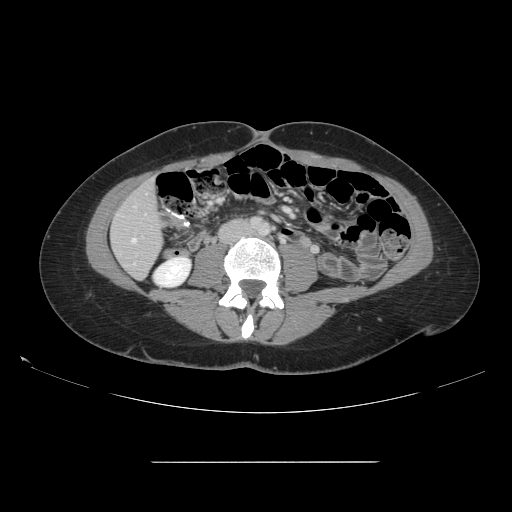
Contrast-enhanced abdominal CT, one axial slice. Slice 31 of 151 in the series (ordered by position). 120 kVp. Intravenous contrast given. Soft-tissue window (W 400 / L 40 HU). 2.5 mm slice thickness. 512 × 512 image matrix, field of view 421 × 421 mm. Female patient, age 46 years. Case-level facts recorded for this patient, not image findings: diagnosis: colorectal cancer liver metastases, imaged before liver resection; multiple liver metastases: yes; largest metastasis: 3 cm.
Annotated regions visible in this slice (manually delineated by an expert):
- hepatic veins: bounding box (x1, y1, x2, y2) in pixels: (132, 239, 136, 242)
- liver: (112, 182, 163, 278)
- planned liver remnant (the part of the liver to remain after resection): (112, 182, 163, 278)